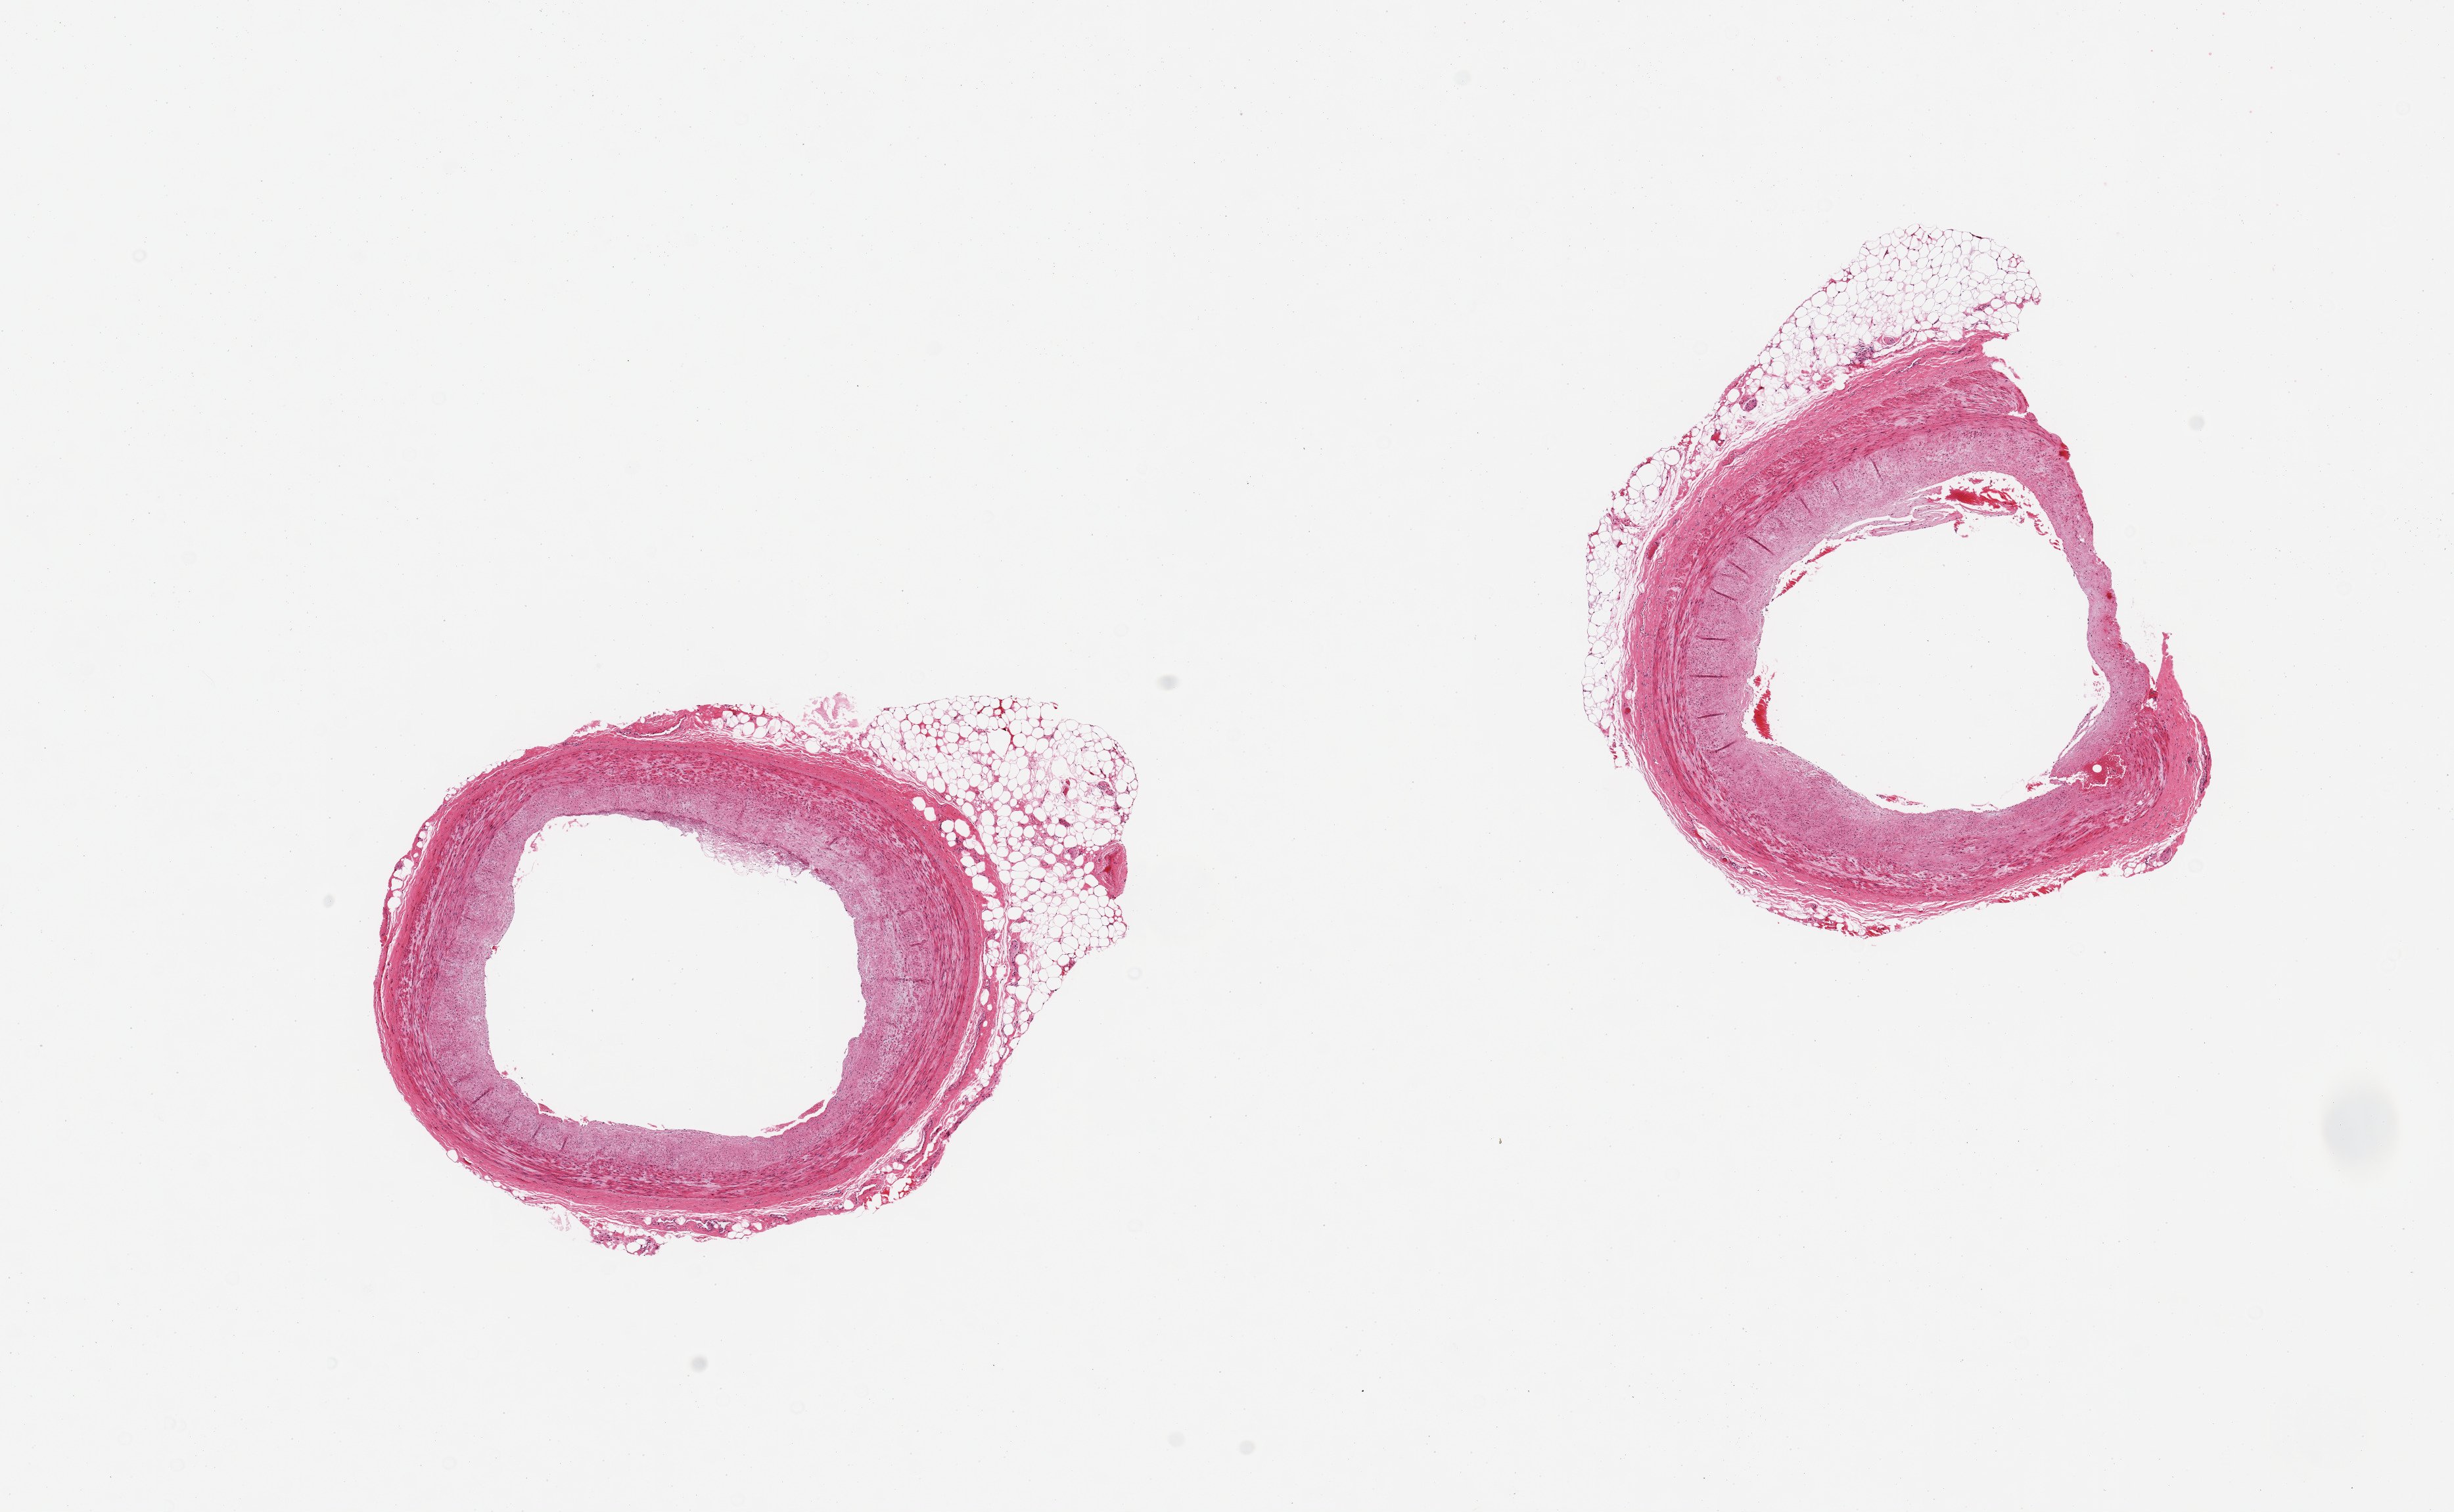
H&E whole-slide image, brightfield, shown as a low-resolution overview of the whole scanned area (about 14.8 x 9.1 mm). PAXgene-fixed paraffin-embedded (PFPE) section. Sampled site (target tissue): coronary artery. Donor tissue sample. Female donor.
Review note (as recorded): 2 pieces, adherent nubbins of fat up to ~1mm; mild atherosis, ~10-15% luminal occlusion.